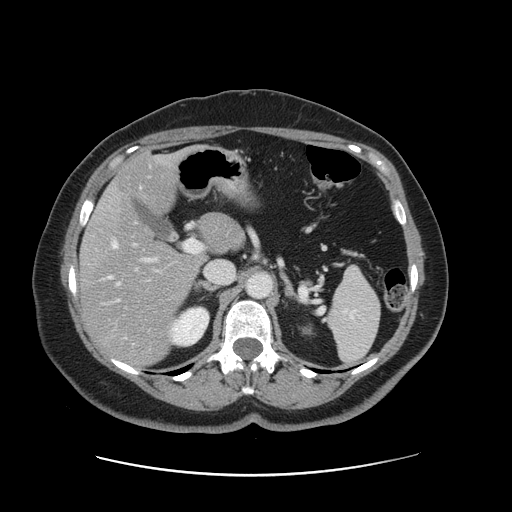
Contrast-enhanced abdominal CT, one axial slice. Slice 84 of 161 in the series (ordered by position). 120 kVp. Intravenous contrast given. Soft-tissue window (W 400 / L 40 HU). 512 × 512 image matrix. Female patient, age 62 years. Case-level facts recorded for this patient, not image findings: diagnosis: colorectal cancer liver metastases, imaged before liver resection; multiple liver metastases: no; largest metastasis: 2.5 cm.
Outlined on this slice (outlined manually by an expert reader):
- hepatic veins: box from (x=109, y=186) to (x=142, y=286) px
- liver: (x=81, y=154)–(x=241, y=365)
- planned liver remnant (the part of the liver to remain after resection): (x=110, y=155)–(x=241, y=253)
- portal vein (with intrahepatic branches): (x=104, y=239)–(x=202, y=304)